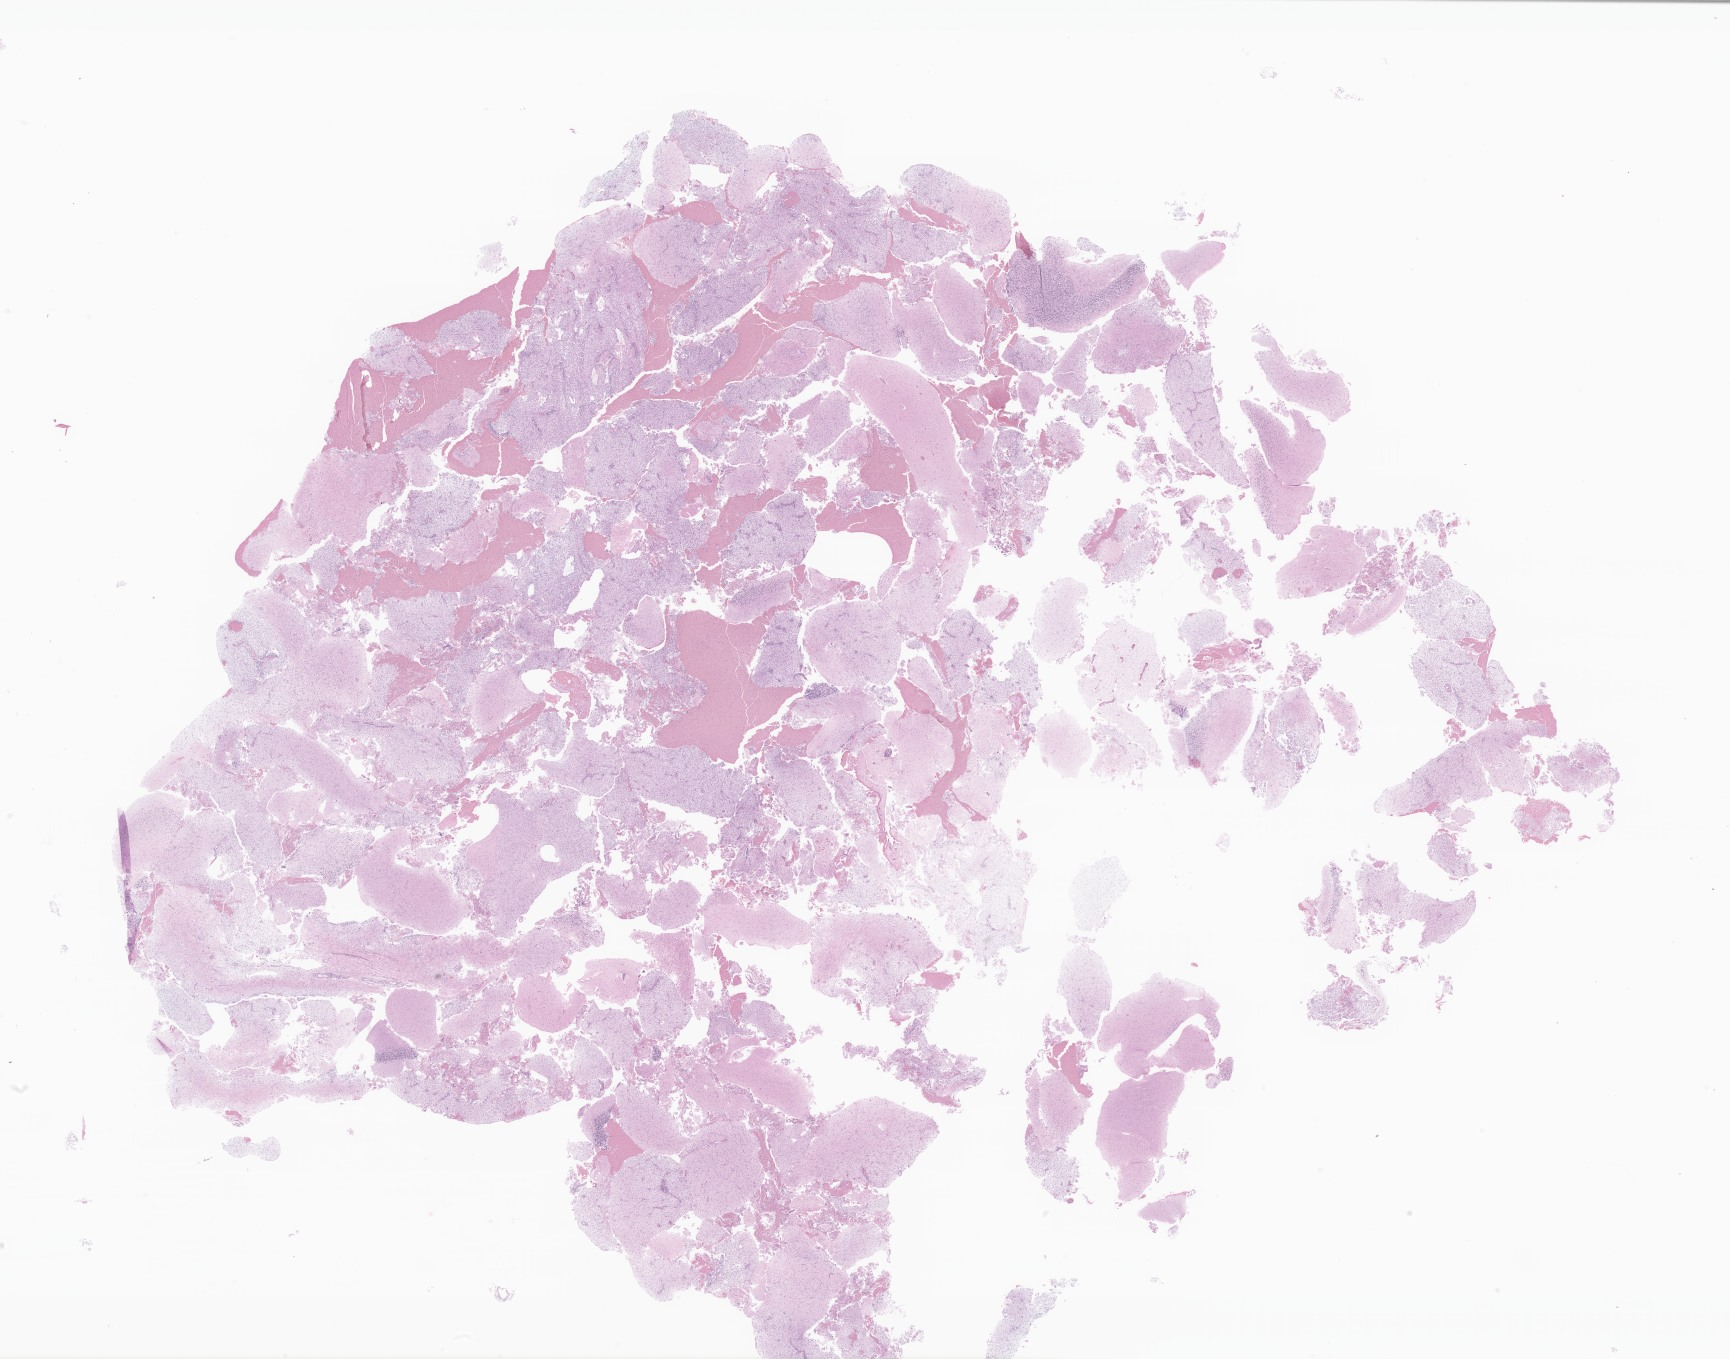
Digitized haematoxylin and eosin-stained section of tumor tissue from the cerebellum — low-resolution overview of the scanned area, about 29.2 x 22.9 mm. Formalin-fixed, paraffin-embedded (FFPE) tissue. Male patient, age 984 days.
Diagnosis: Pilocytic astrocytoma.